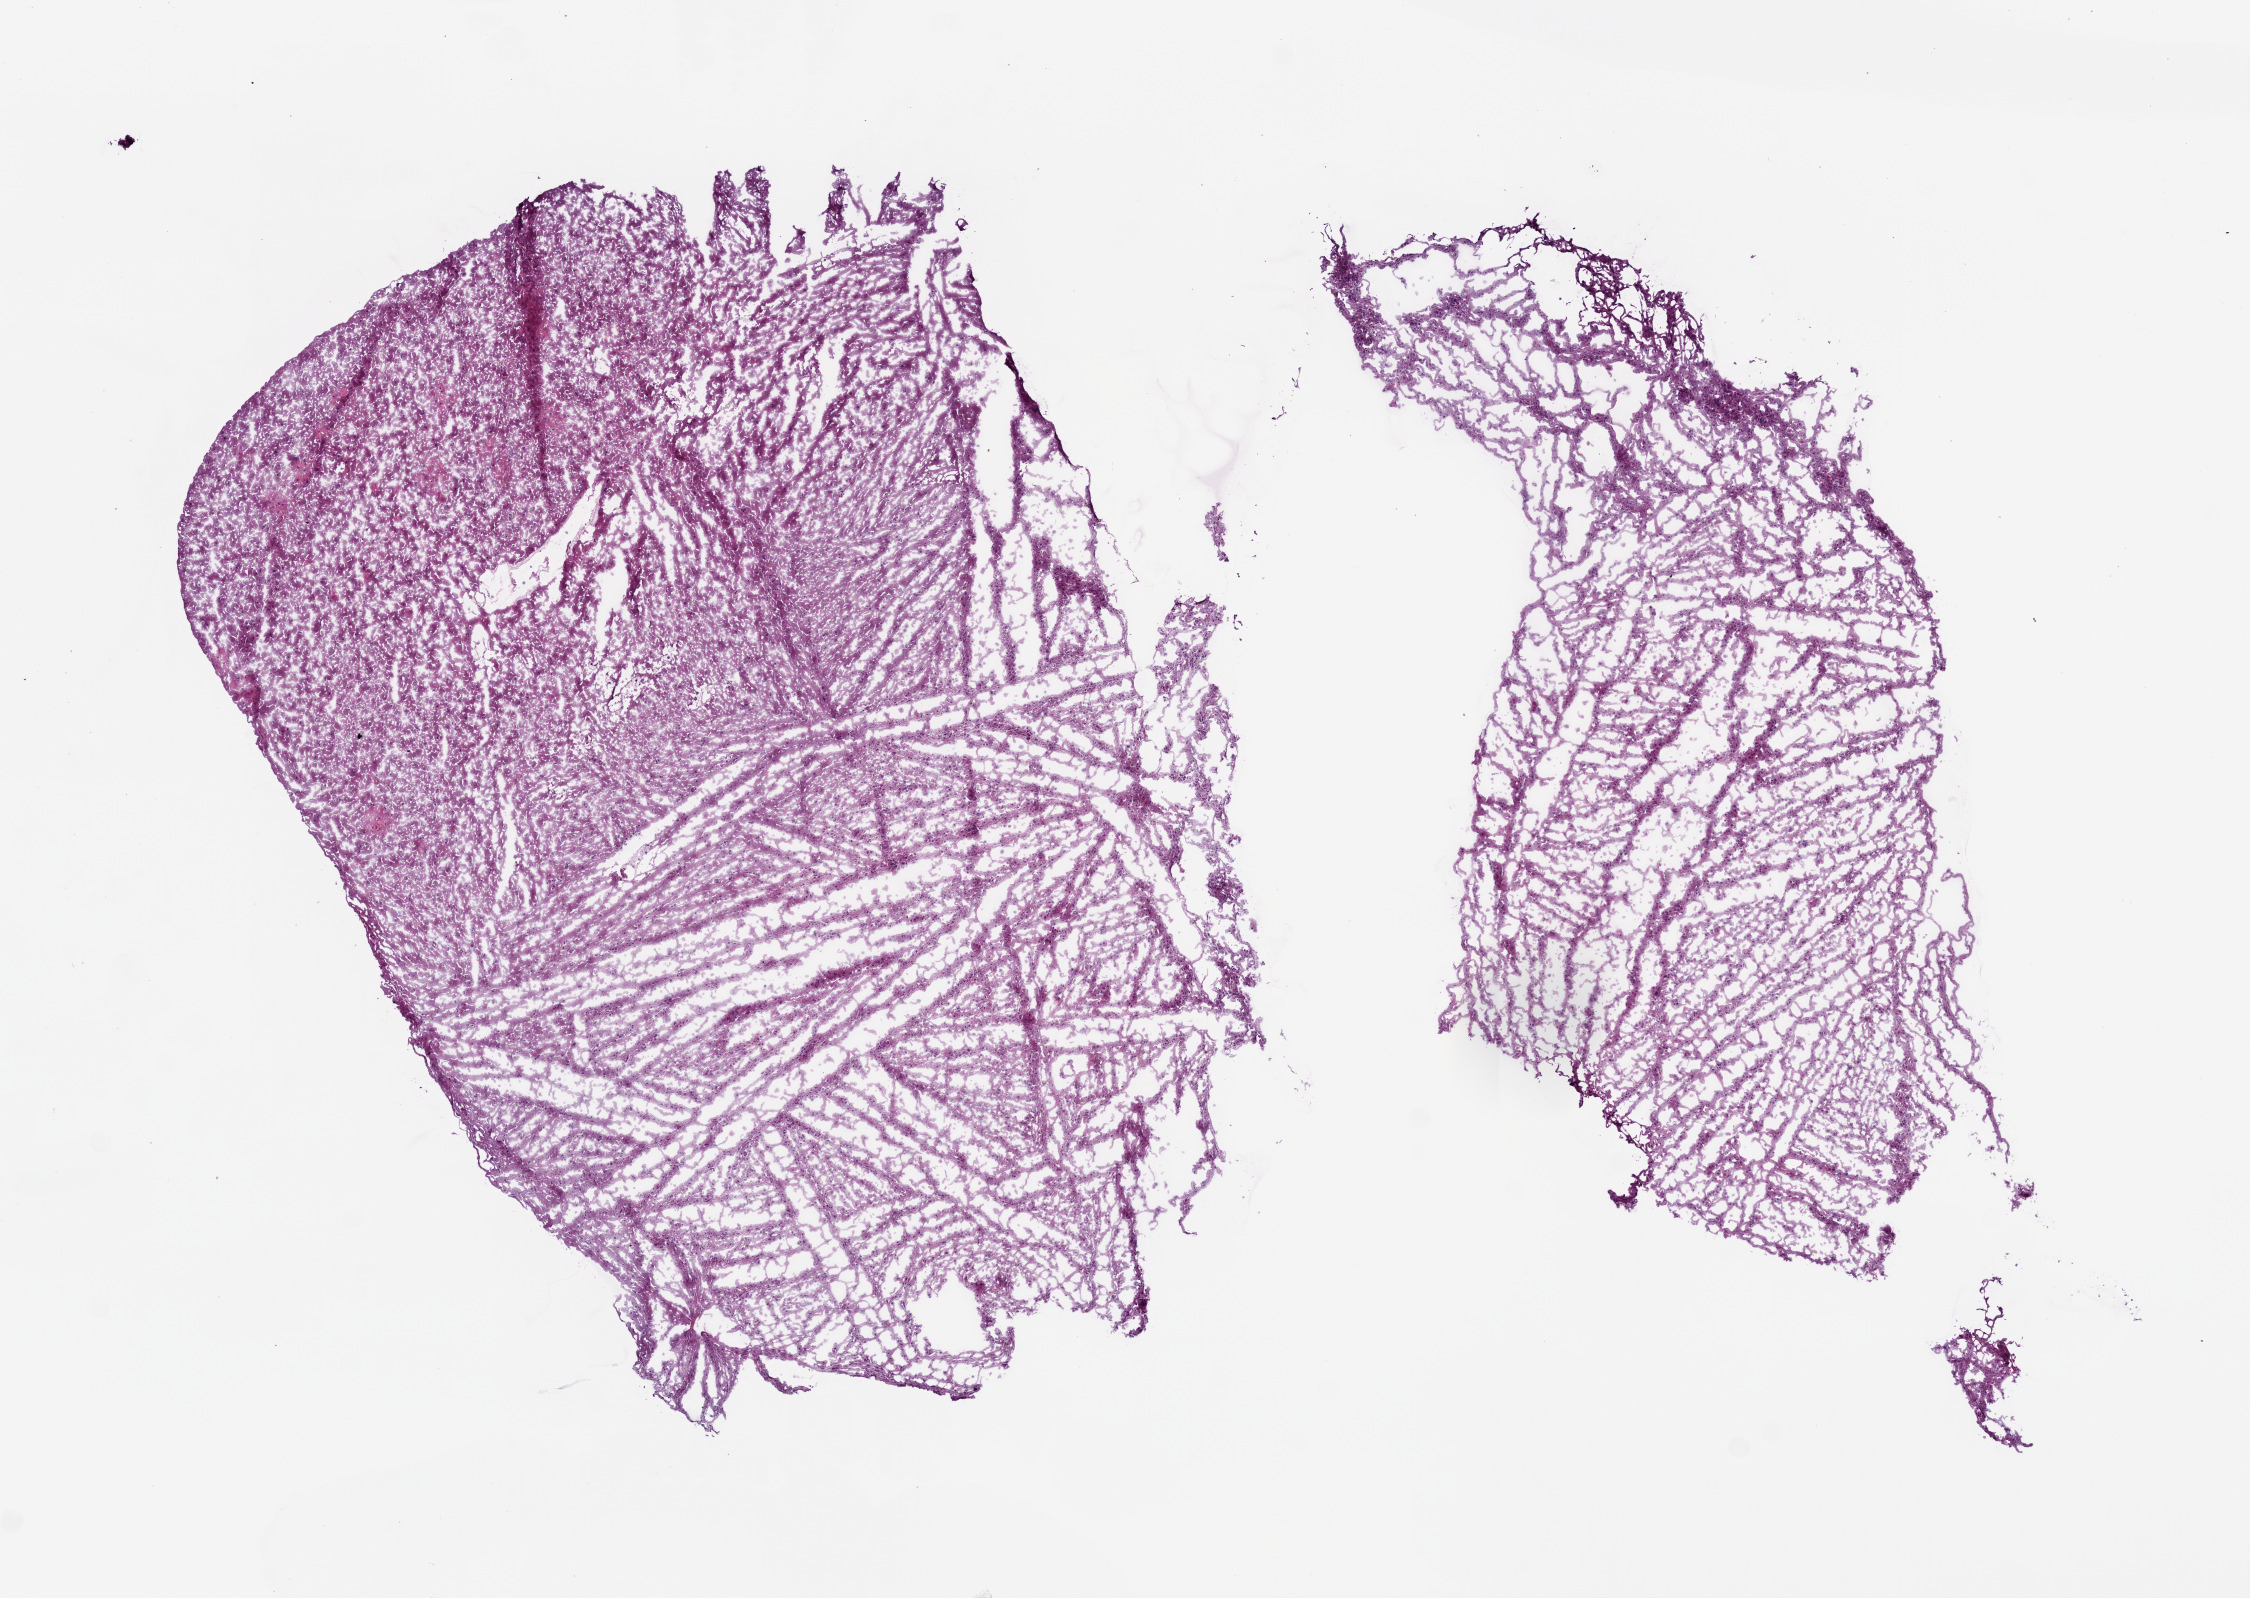
H&E-stained whole-slide image — a low-resolution overview of the entire scanned area, about 9.0 x 6.4 mm; frozen section from the bottom of the tissue portion; brain, primary tumour sample. Patient: female, age at initial diagnosis 44 years. Histologic grade: G3 (poorly differentiated). Slide review estimates, as recorded: tumour cells 100%, tumour nuclei 60%, normal cells 0%, stromal cells 0%, necrosis 0%.
Pathologic diagnosis: Astrocytoma, anaplastic.